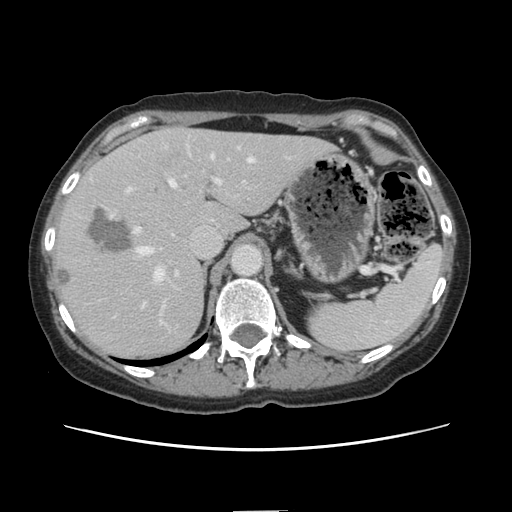
Contrast-enhanced abdominal CT, one axial slice; slice 98 of 141 in the series (ordered by position); 120 kVp; intravenous contrast given; soft-tissue window (W 400 / L 40 HU); 512 × 512 image matrix, field of view 350 × 350 mm. Female patient, age 63 years. Case-level facts recorded for this patient, not image findings: diagnosis: colorectal cancer liver metastases, imaged before liver resection; multiple liver metastases: yes; largest metastasis: 3.2 cm; chemotherapy before resection: yes.
Structures marked on this image (expert manual segmentation):
- hepatic veins: bounding box [x1, y1, x2, y2] px = [138, 155, 254, 281]
- liver: [50, 129, 331, 360]
- planned liver remnant (the part of the liver to remain after resection): [184, 129, 331, 237]
- portal vein (with intrahepatic branches): [126, 178, 222, 275]